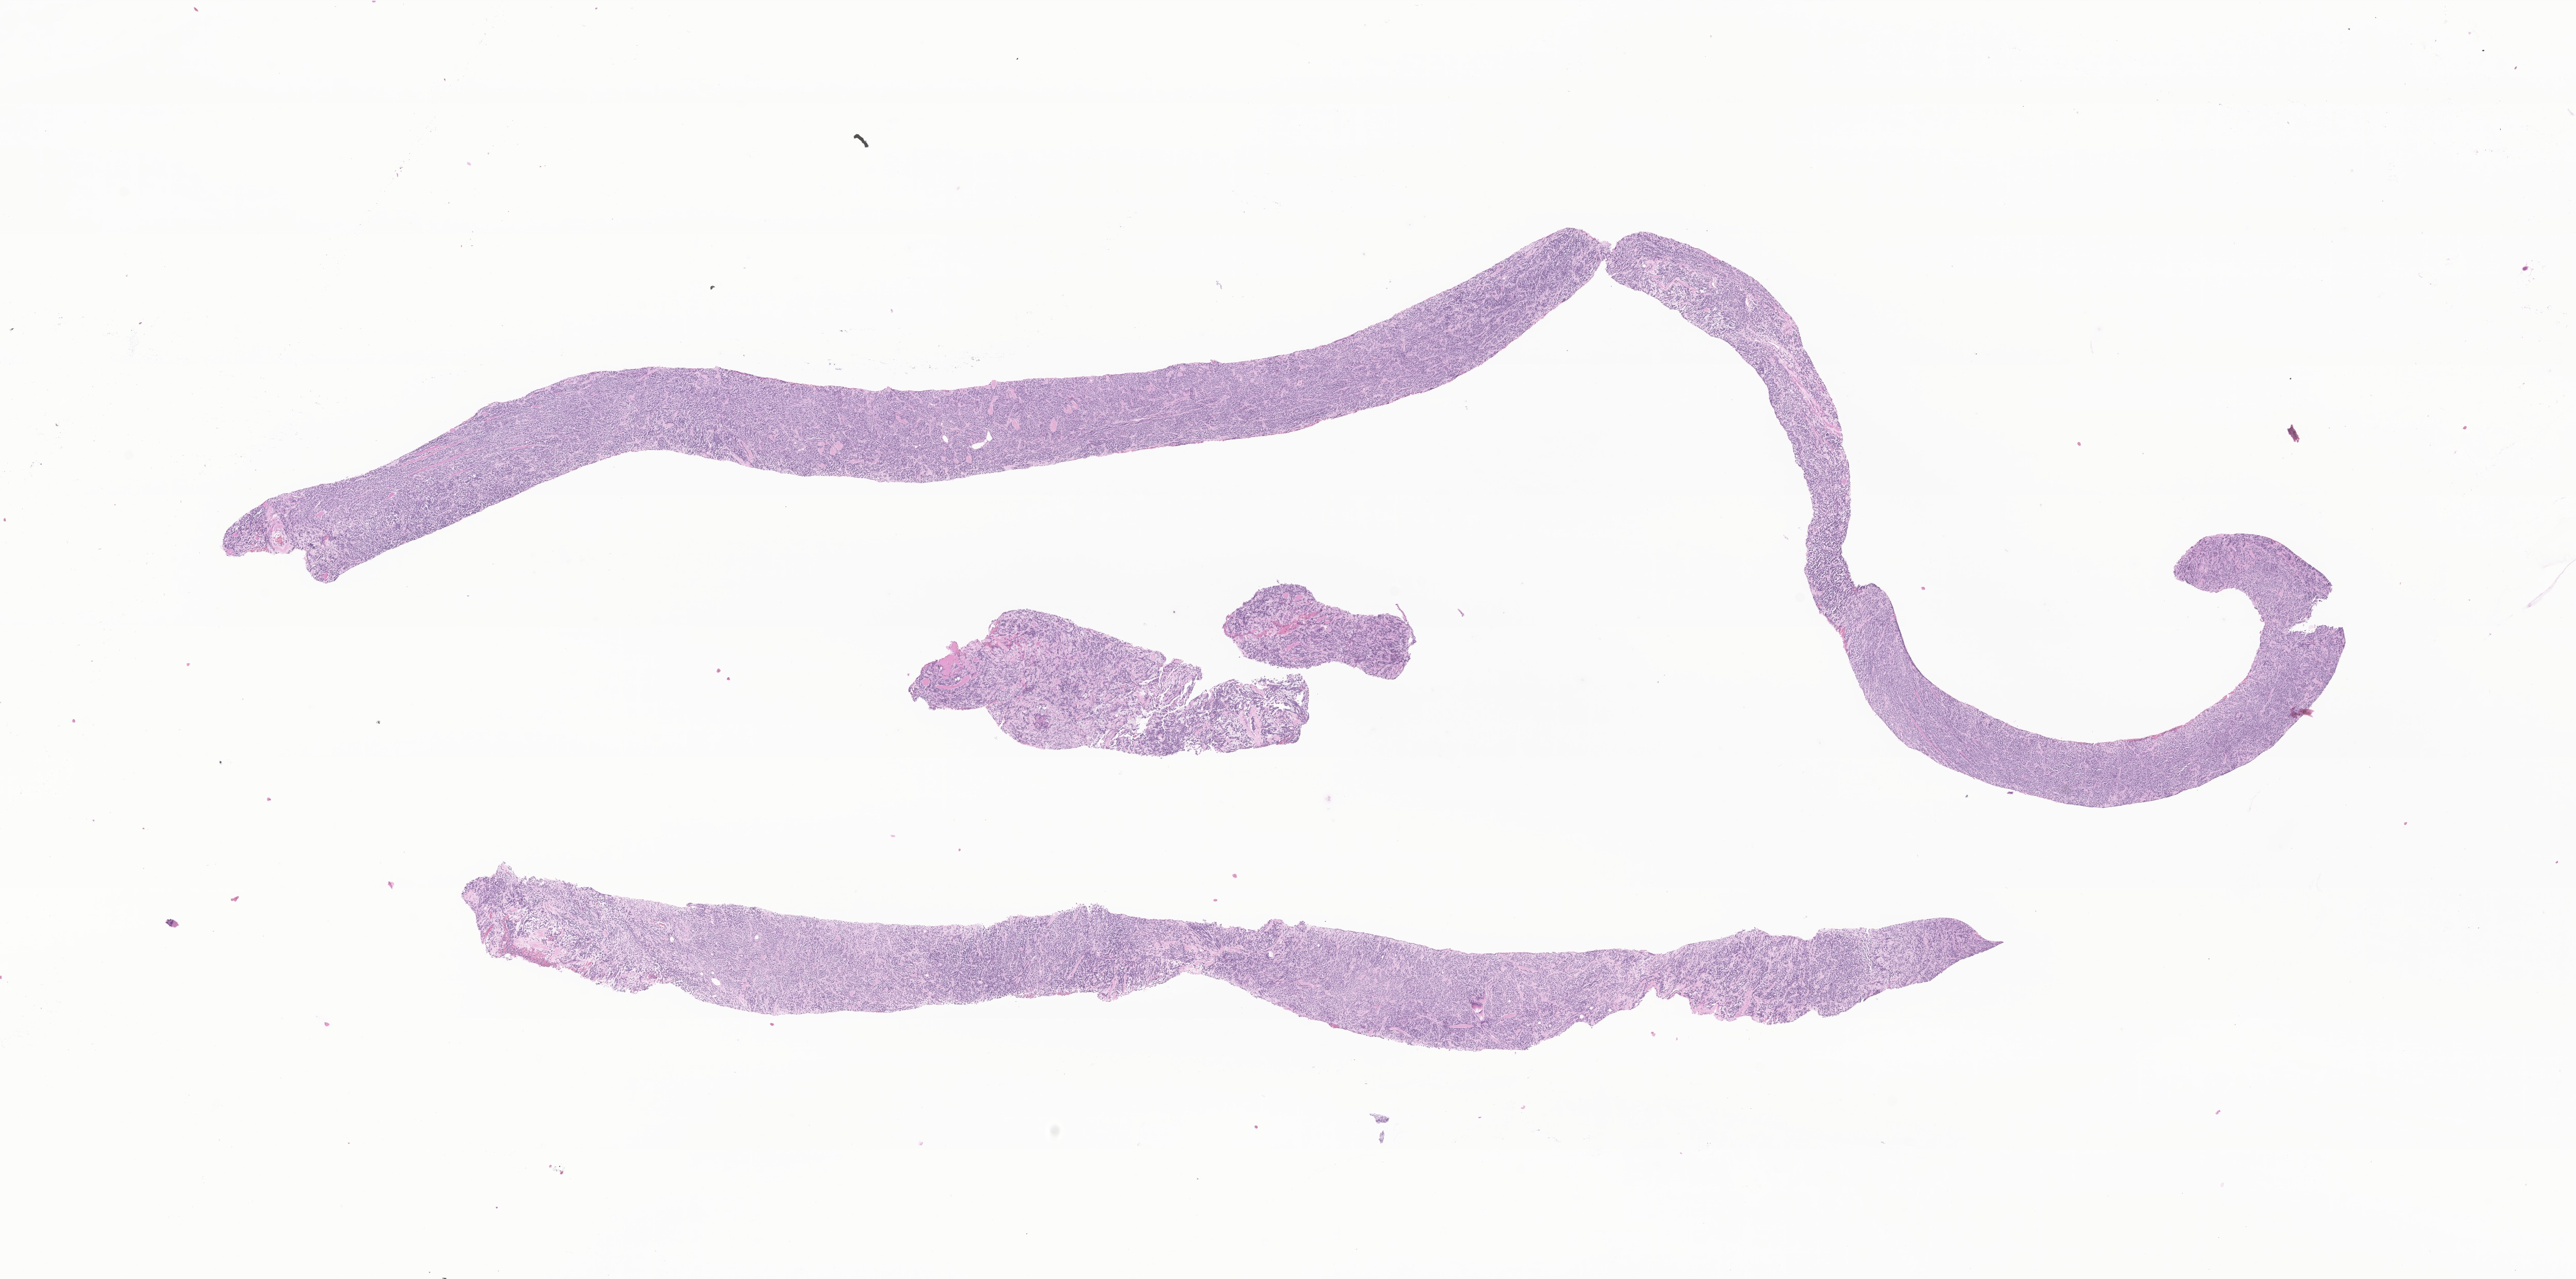
Whole-slide image, H&E stain of tumor tissue from the soft tissue of abdomen, low-resolution overview of the scanned area, about 21.0 x 10.4 mm, FFPE section. Male patient, age 208 months (17 years 4 months).
• diagnosis: Small cell sarcoma